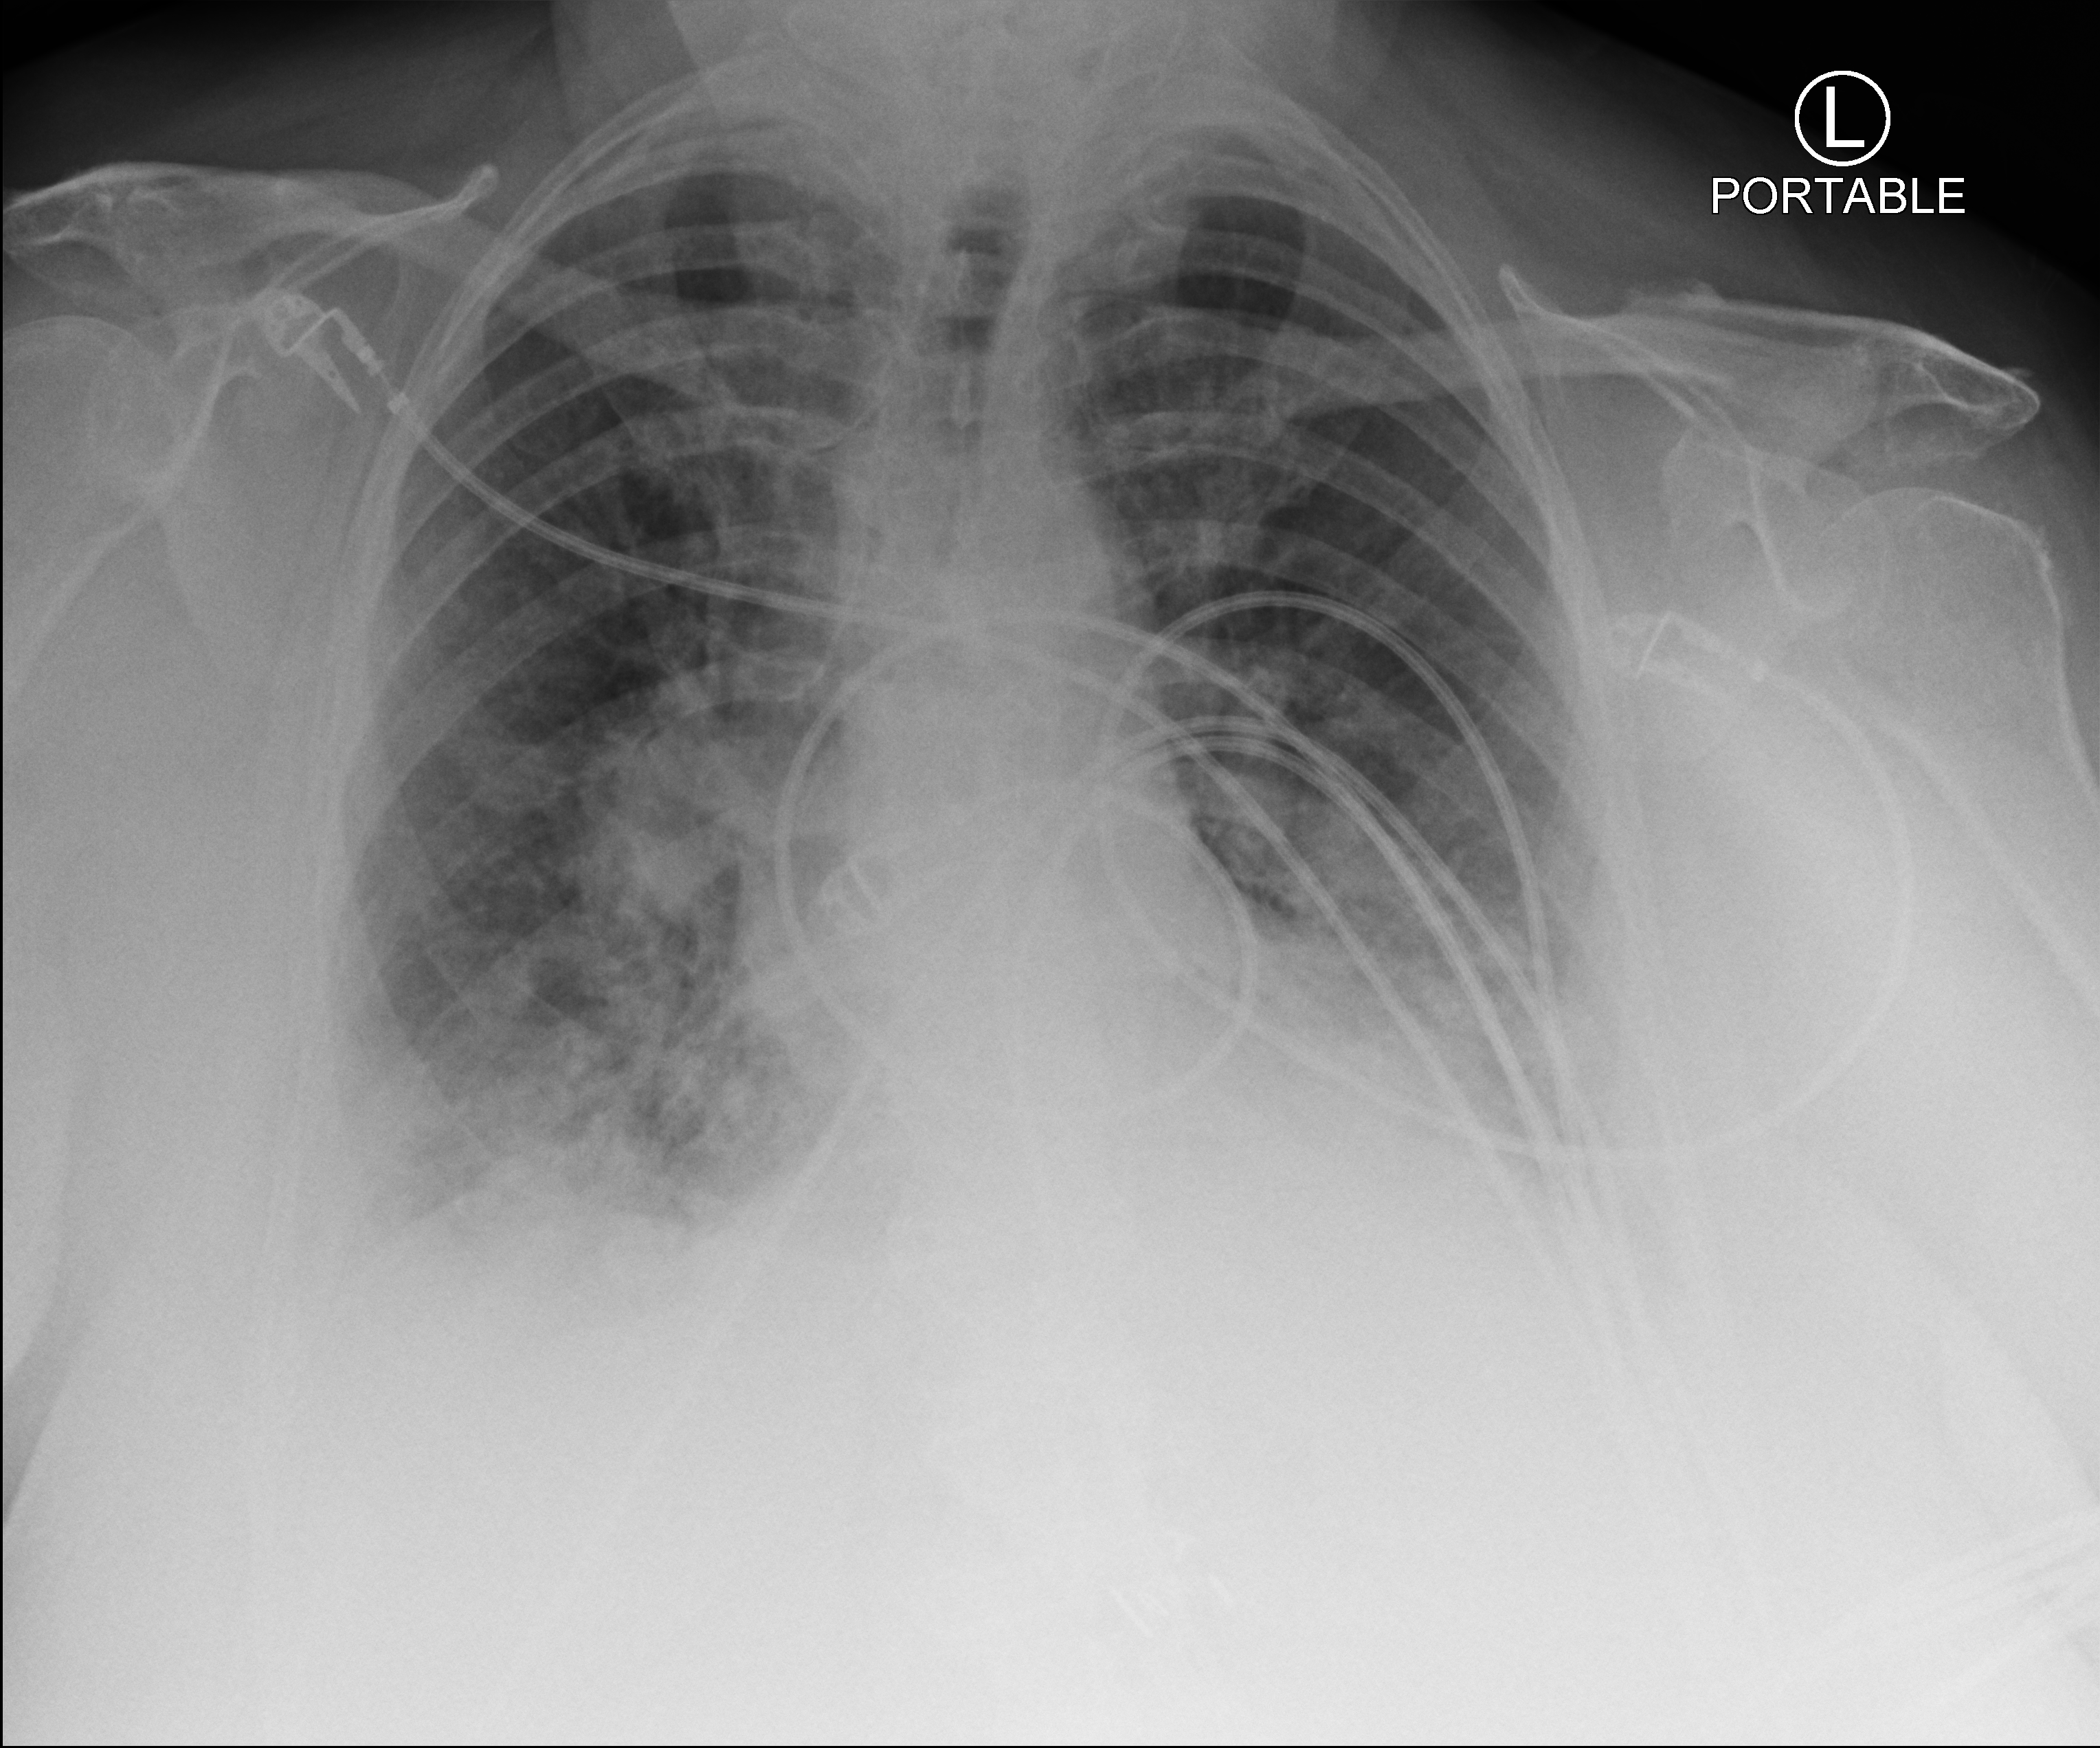
Chest X-ray (portable); anteroposterior (AP) projection. Female patient hospitalised with COVID-19, age 75–90 years.
From the hospital-stay record, not from the radiograph (when in the stay this image was taken is not recorded): smoking status (admission record): never; mechanically ventilated during this hospital stay: no.